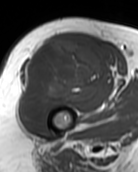
MRI of an extremity soft-tissue mass, one axial slice; MR volume resampled by the dataset authors to the PET/CT grid (not the native acquisition matrix); 3.27 mm slice thickness; 138 × 172 image matrix, field of view 135 × 168 mm. Female patient. From the clinical record (not read from this slice): histological type: pleiomorphic undifferentiated sarcoma; grade: high; site of the primary tumour: right quadricep.
Annotated regions visible in this slice (expert contour drawn on MRI and transferred to this co-registered scan by the dataset authors):
- gross tumour volume including surrounding oedema: box from (x=19, y=39) to (x=109, y=124) px
- gross tumour volume (mass): (x=19, y=39)–(x=109, y=124)